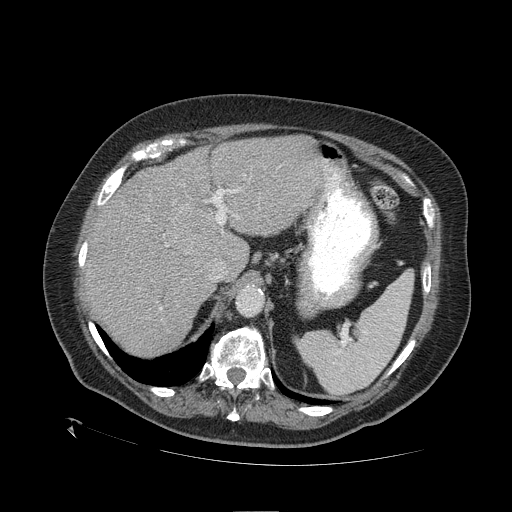
Contrast-enhanced abdominal CT (liver protocol), one axial slice; position 77 of 109 along the scan axis; reconstruction kernel STANDARD; 120 kVp; one of 2 acquisitions stored at this slice position; soft-tissue window (W 400 / L 40 HU); 512 × 512 image matrix. From the clinical record (not read from this slice): diagnosis: hepatocellular carcinoma (patient treated with transarterial chemoembolisation; whether this scan precedes or follows treatment is not stated here); TNM stage (as recorded): Stage-I; Child-Pugh class: A; tumour differentiation: no biopsy; tumour size: 4.6 cm.
Outlined on this slice (semi-automatically segmented with operator editing):
- liver parenchyma outside the tumour (the mass and vessels are separate outlines, so this box may not span the whole liver): box from (x=84, y=136) to (x=344, y=356) px
- mass: (x=169, y=205)–(x=212, y=255)
- liver vessels: (x=147, y=167)–(x=340, y=309)